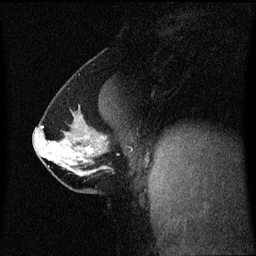
Breast MRI (dynamic contrast-enhanced), one sagittal slice; slice 33 of 60 in the series (ordered by position); dynamic contrast-enhanced series, image 2 of 3 at this slice position (ordered by acquisition); 1.5 T; TE 4.2 ms, TR 8.4 ms; 256 × 256 image matrix, field of view 210 × 210 mm. Patient: female, 40 years. From the clinical record (not read from this slice): setting: breast cancer imaged before/during neoadjuvant chemotherapy; receptor status: triple-negative.
Structures marked on this image (semi-automatically segmented with operator editing):
- analysis volume of interest (the breast-tissue region the enhancement analysis was run in; not a lesion): bounding box <34,112,113,188> (left, top, right, bottom; pixels)
- tumour enhancement mask (voxels above the 70 % enhancement threshold inside the analysis volume of interest): <55,138,108,157>